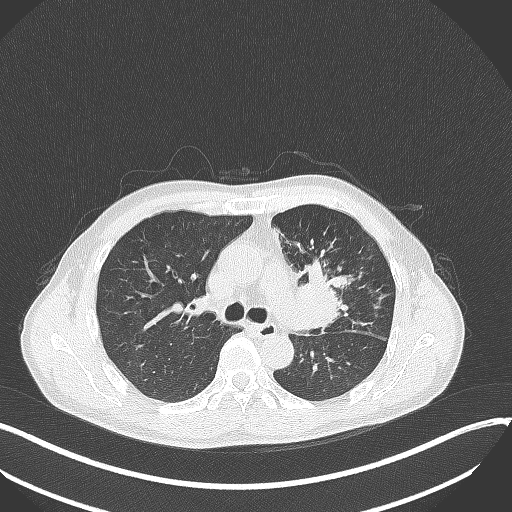
Chest CT, one axial slice. Slice 217 of 411 in the series (ordered by position). 120 kVp. Lung window (W 1500 / L -600 HU). 512 × 512 image matrix. Male patient, age 56 years. From the clinical record (not read from this slice): clinical TNM (as recorded): T2a N0 M0.
Outlined on this slice (rectangle marked by the reading radiologist):
- lung tumour (recorded histology: squamous cell carcinoma): bounding box (x1, y1, x2, y2) in pixels: (286, 258, 352, 336)